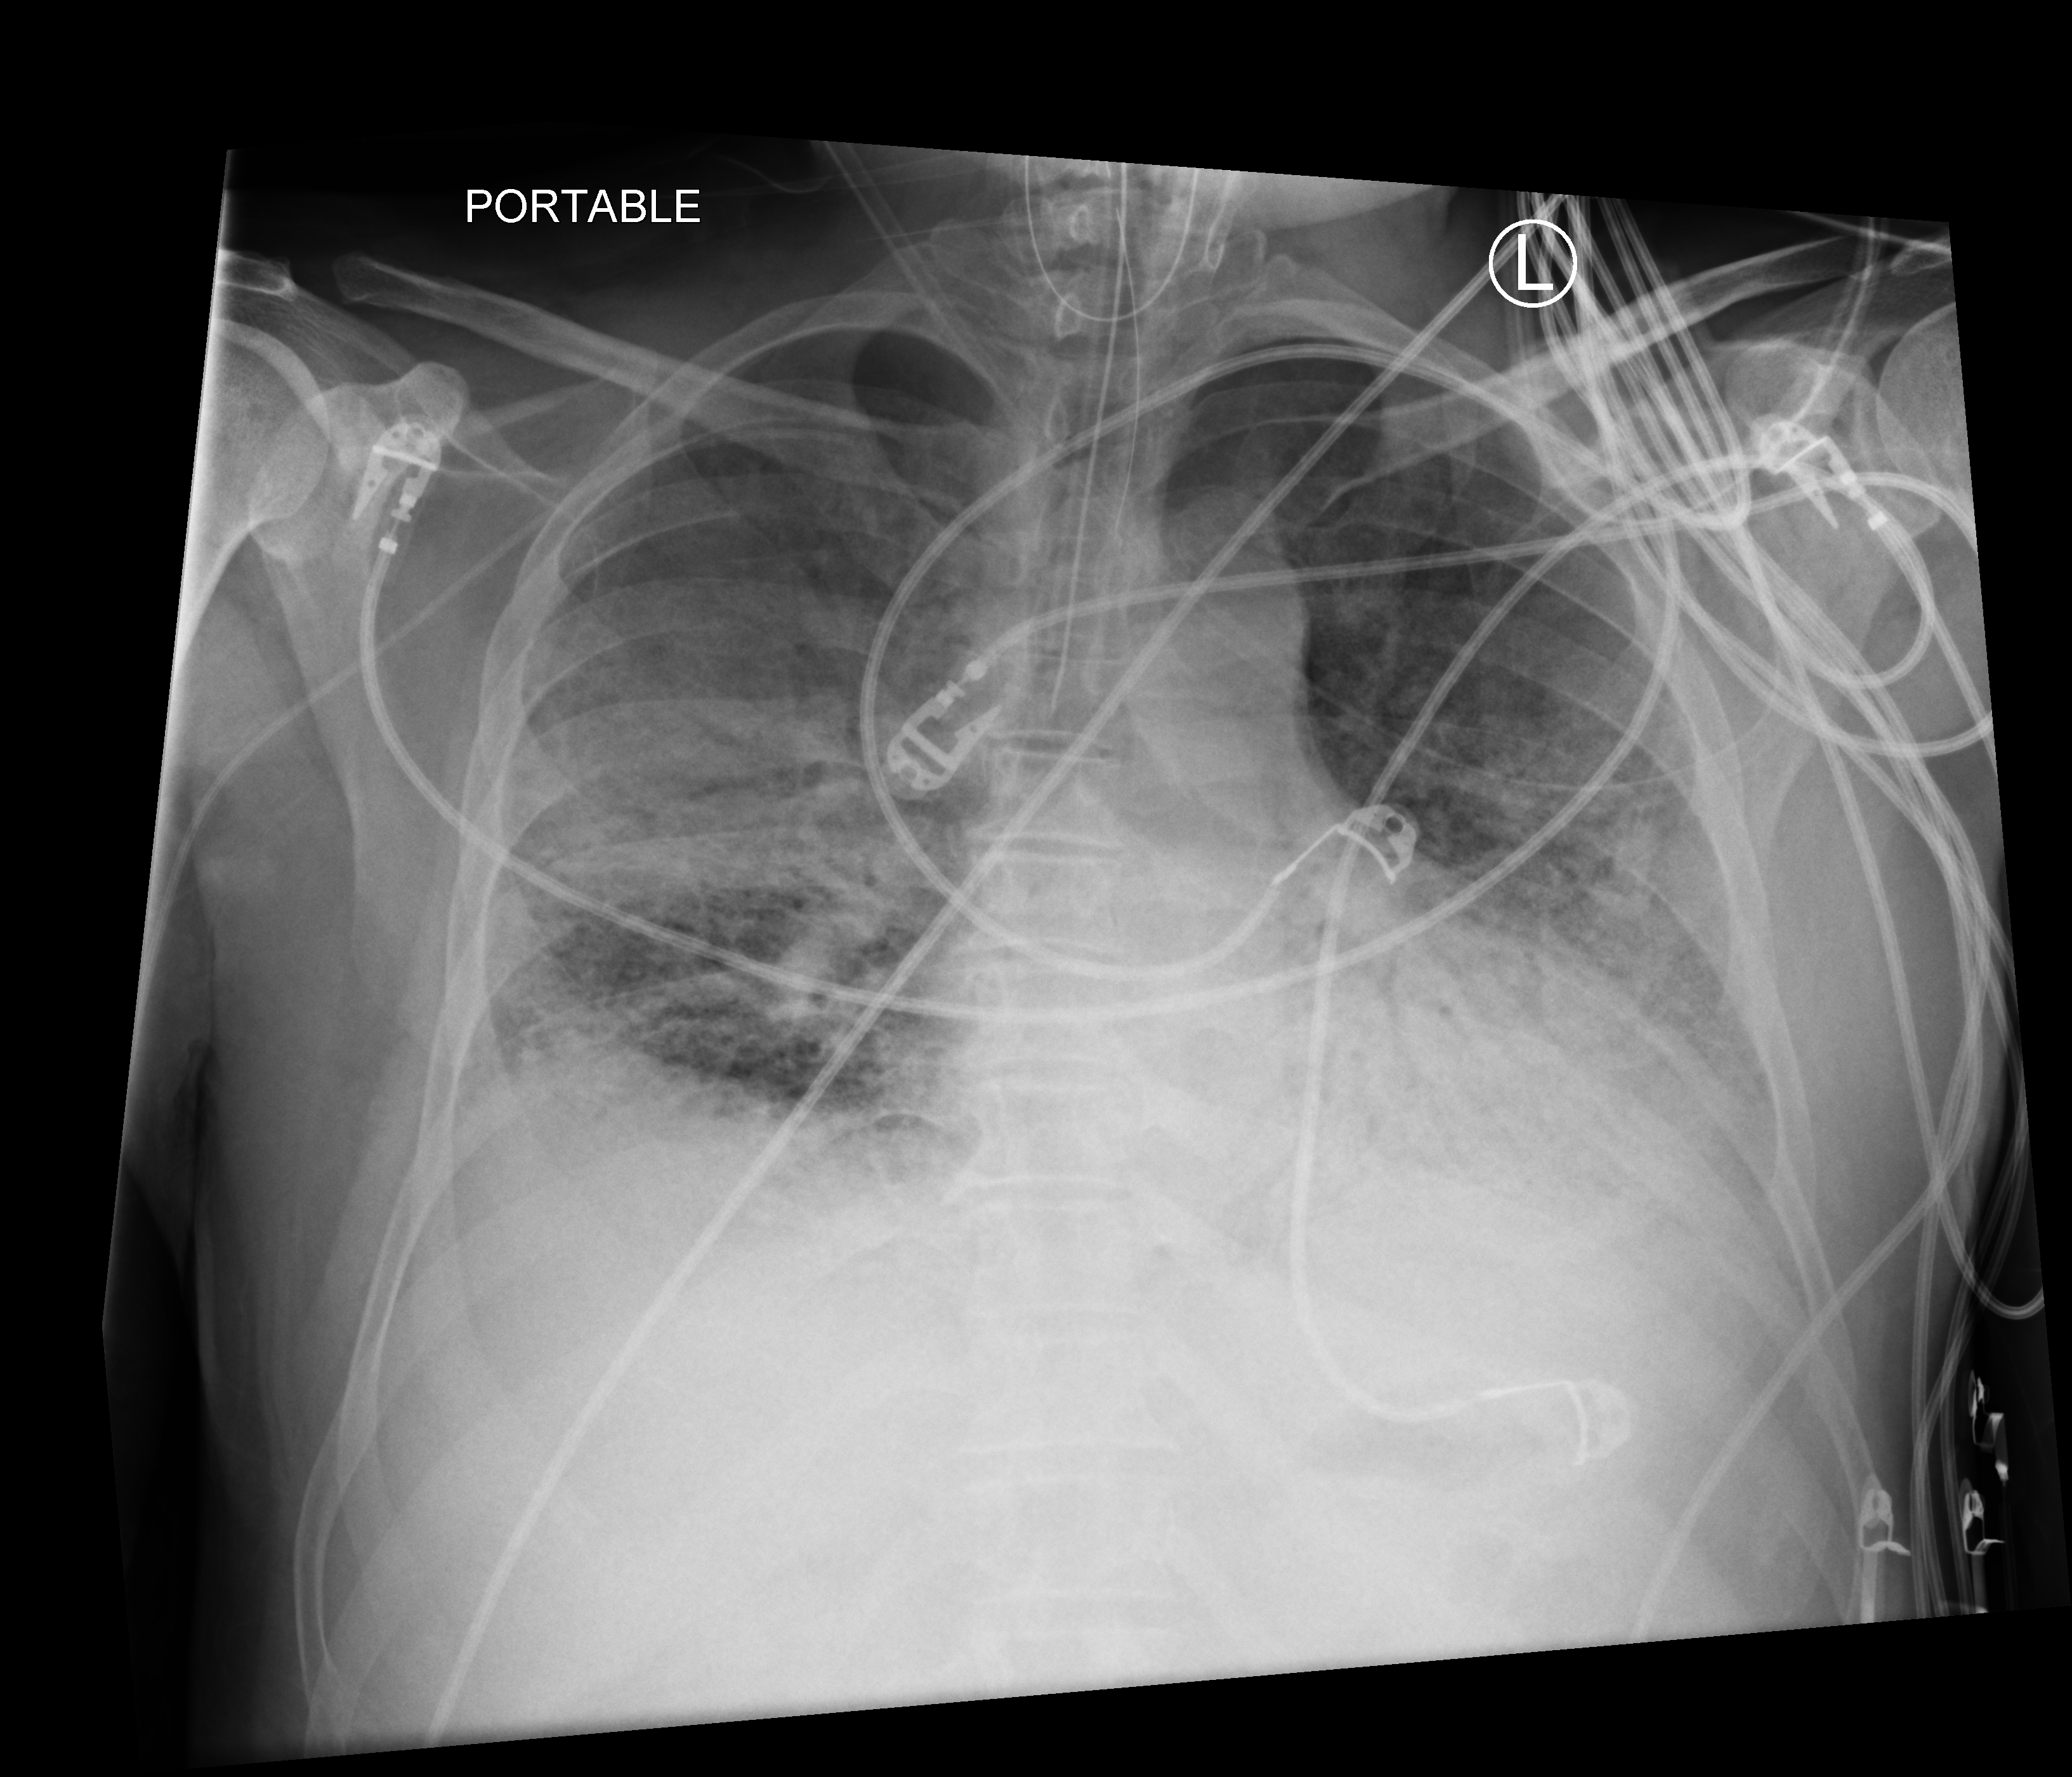
Portable chest radiograph. Patient hospitalised with COVID-19; male, aged 18–59 years.
Hospital-stay facts (about this admission, not read from this image; timing relative to this image not recorded): chronic kidney disease (admission record): no.